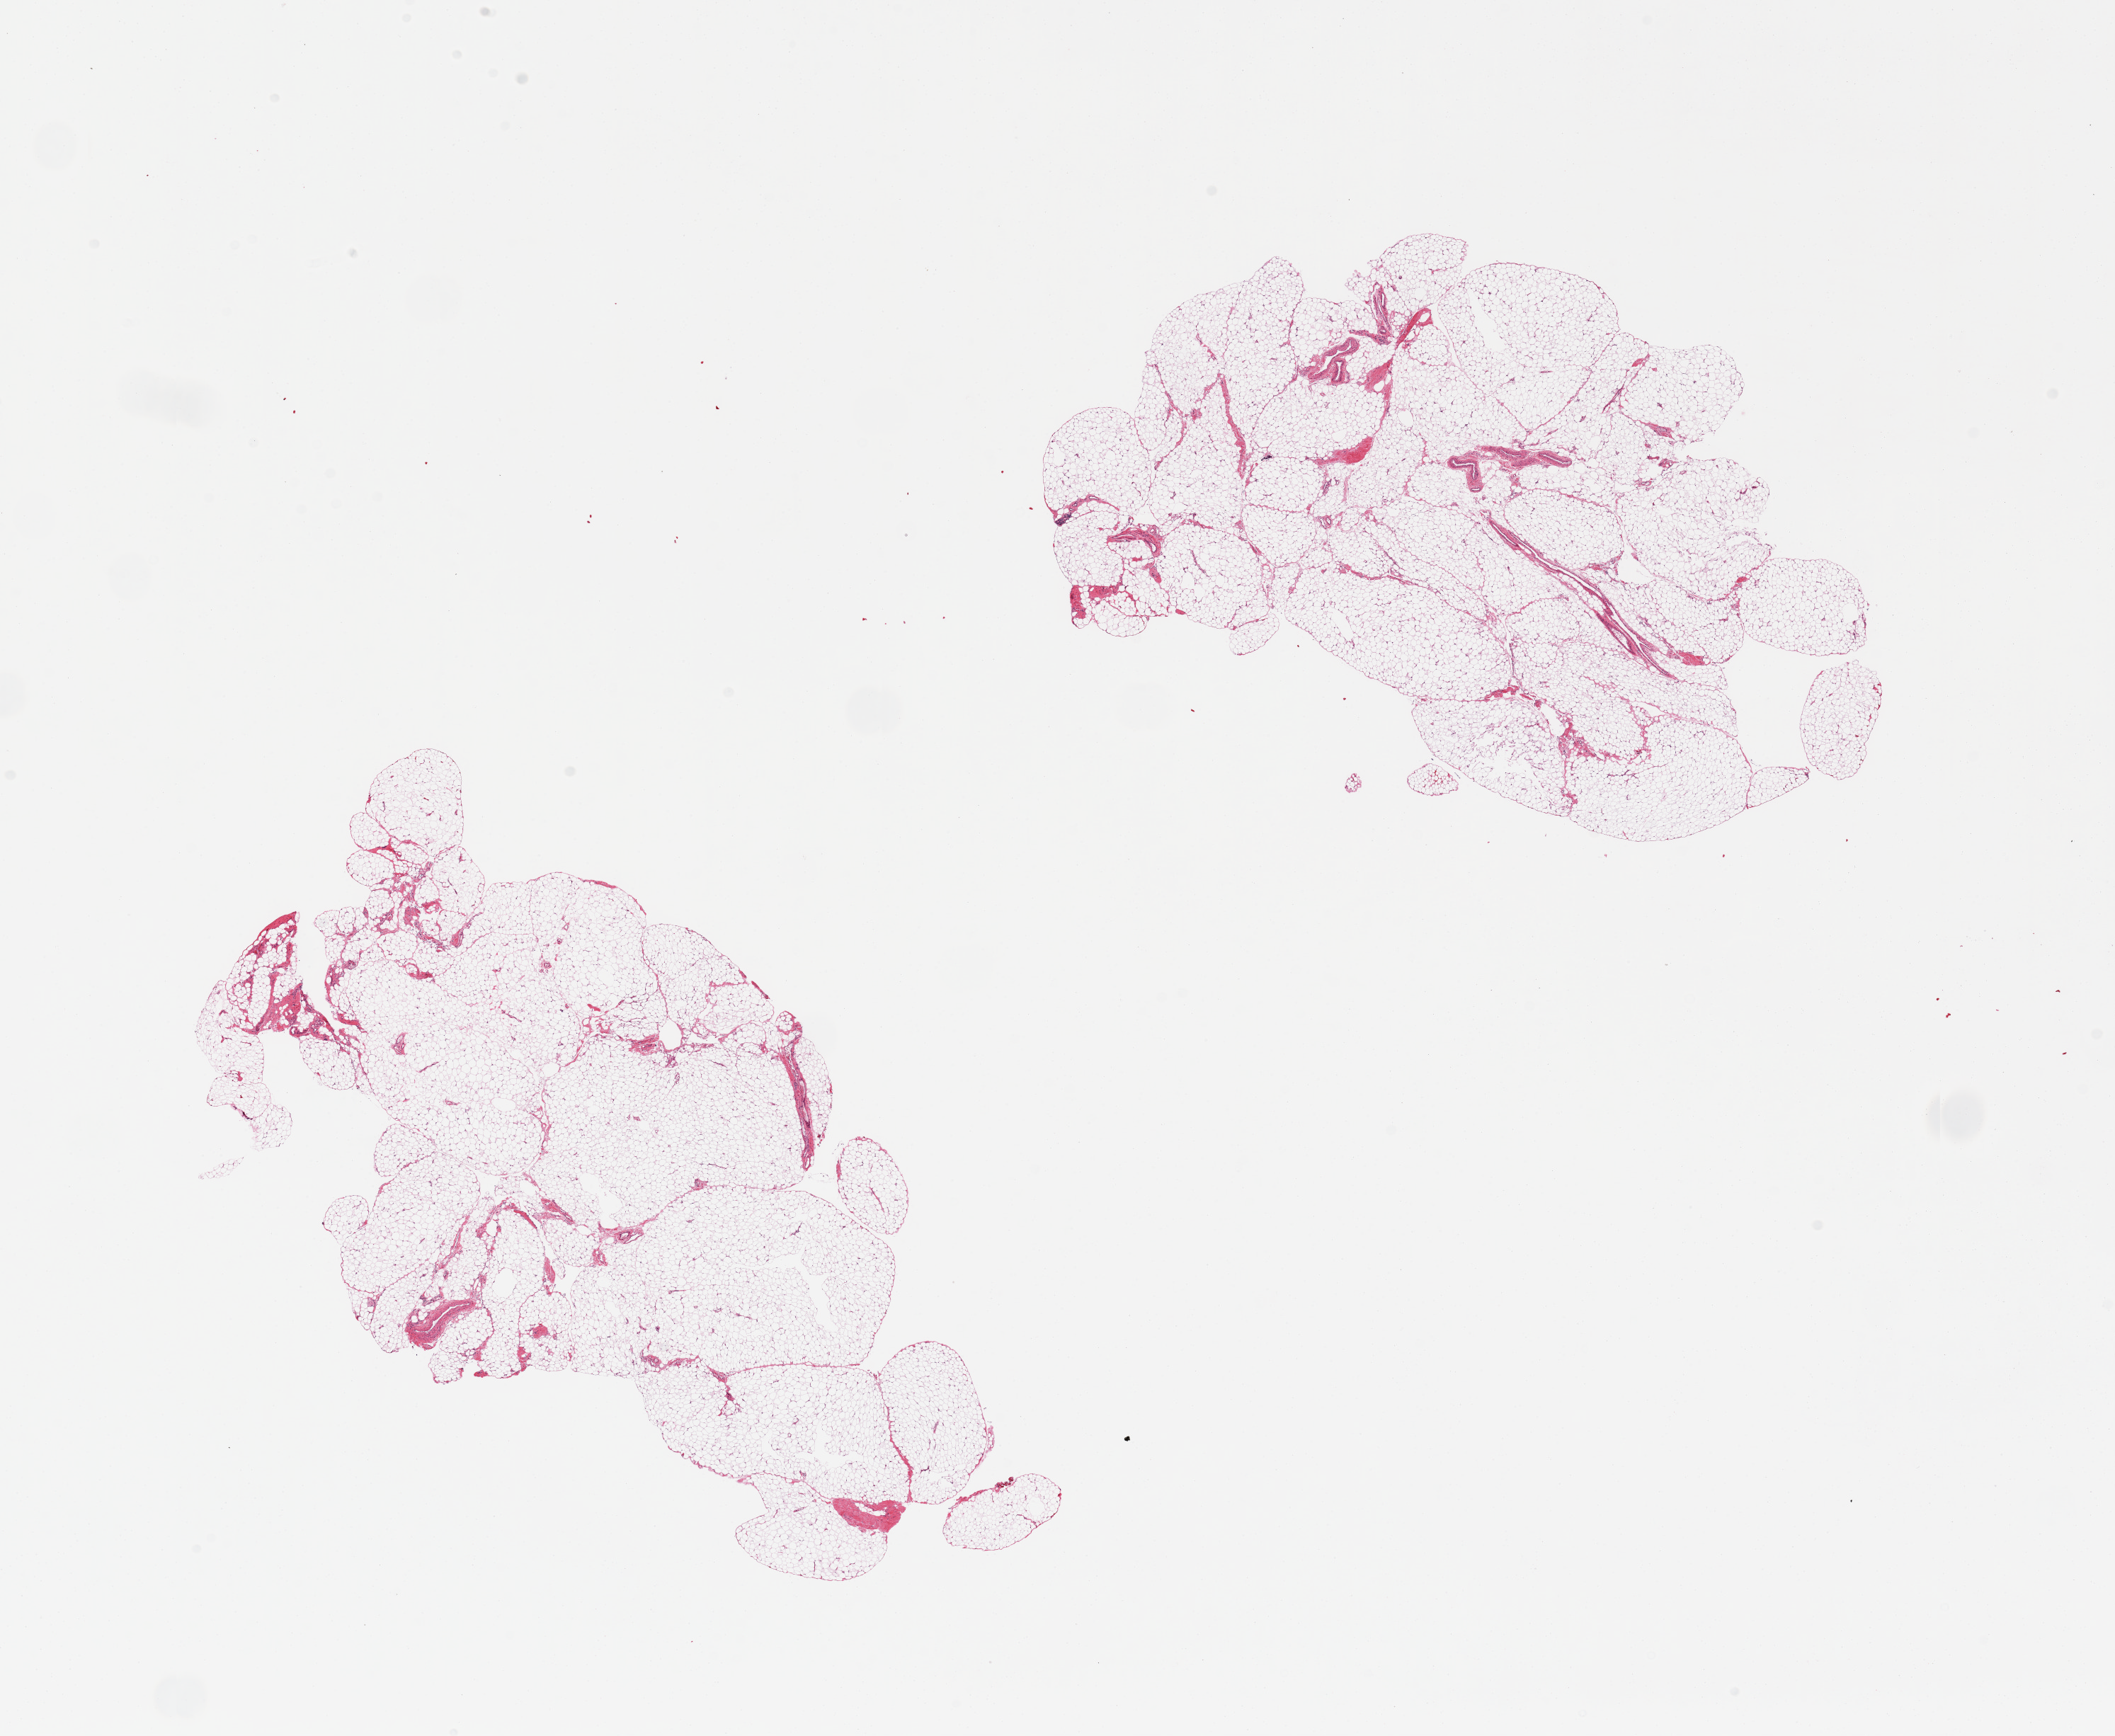
Haematoxylin and eosin whole-slide image, brightfield — shown as a low-resolution overview of the whole scanned area (about 23.6 x 19.4 mm, from a 20x scan); PAXgene-fixed, paraffin-embedded tissue; sampled site (target tissue): omentum; donor tissue sample. Donor sex: female.
Reviewer comment on this tissue sample: 2 pieces.